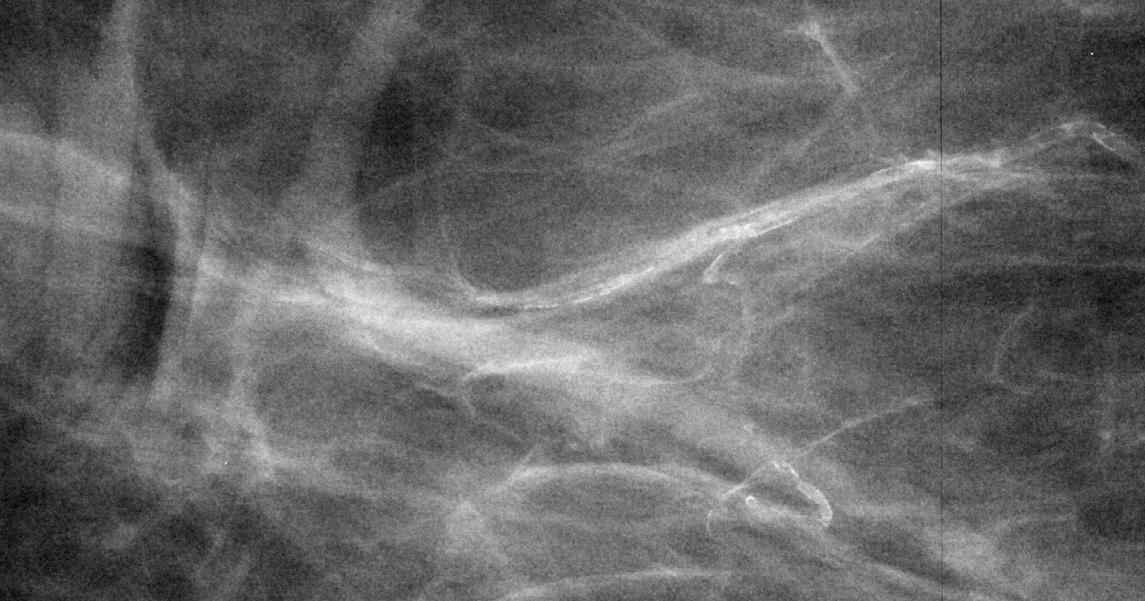
Region of interest cut from a scanned film mammogram (one marked finding); right breast; CC view; BI-RADS breast density category 1 (scale 1–4).
- Marked abnormality: calcifications, morphology vascular; BI-RADS assessment category 2; subtlety rating 4 on a 1 (subtle) to 5 (obvious) scale; benign without callback (not worked up further).